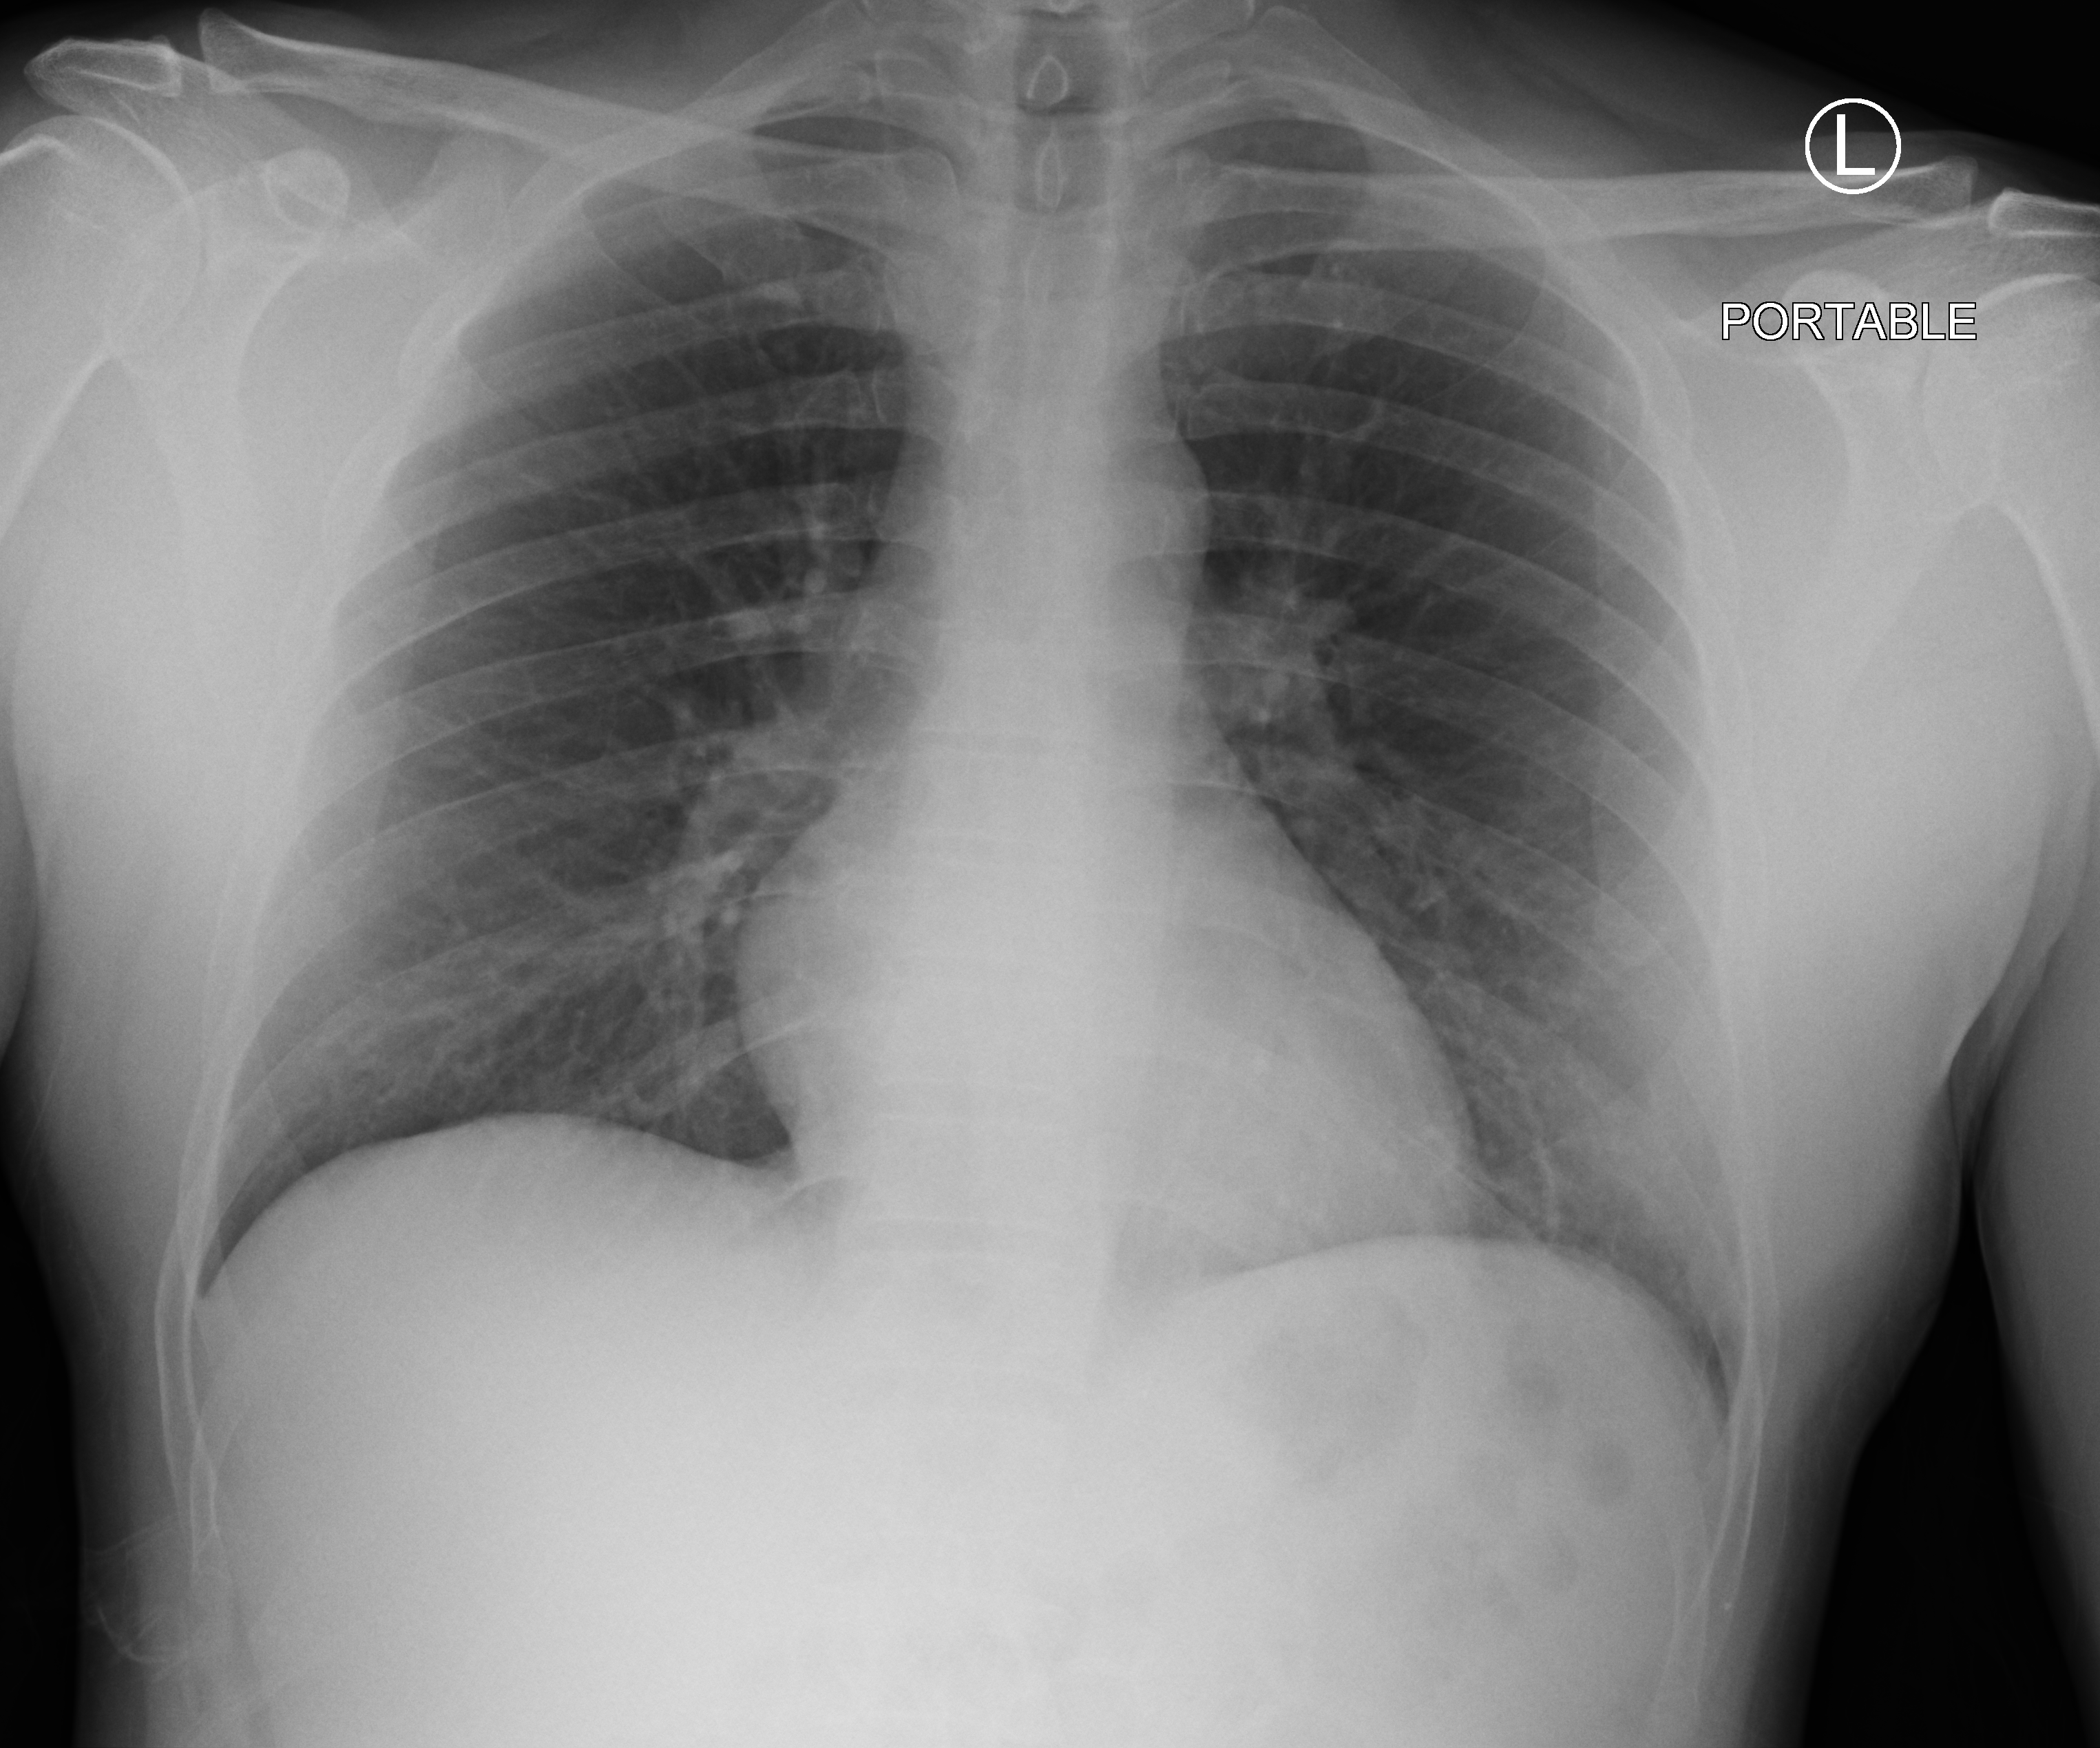
Portable chest radiograph; anteroposterior (AP) projection. Male patient hospitalised with COVID-19, age 18–59 years.
Admission-level facts for this patient (not findings on this image; timing relative to this image not recorded): mechanically ventilated during this hospital stay: no.